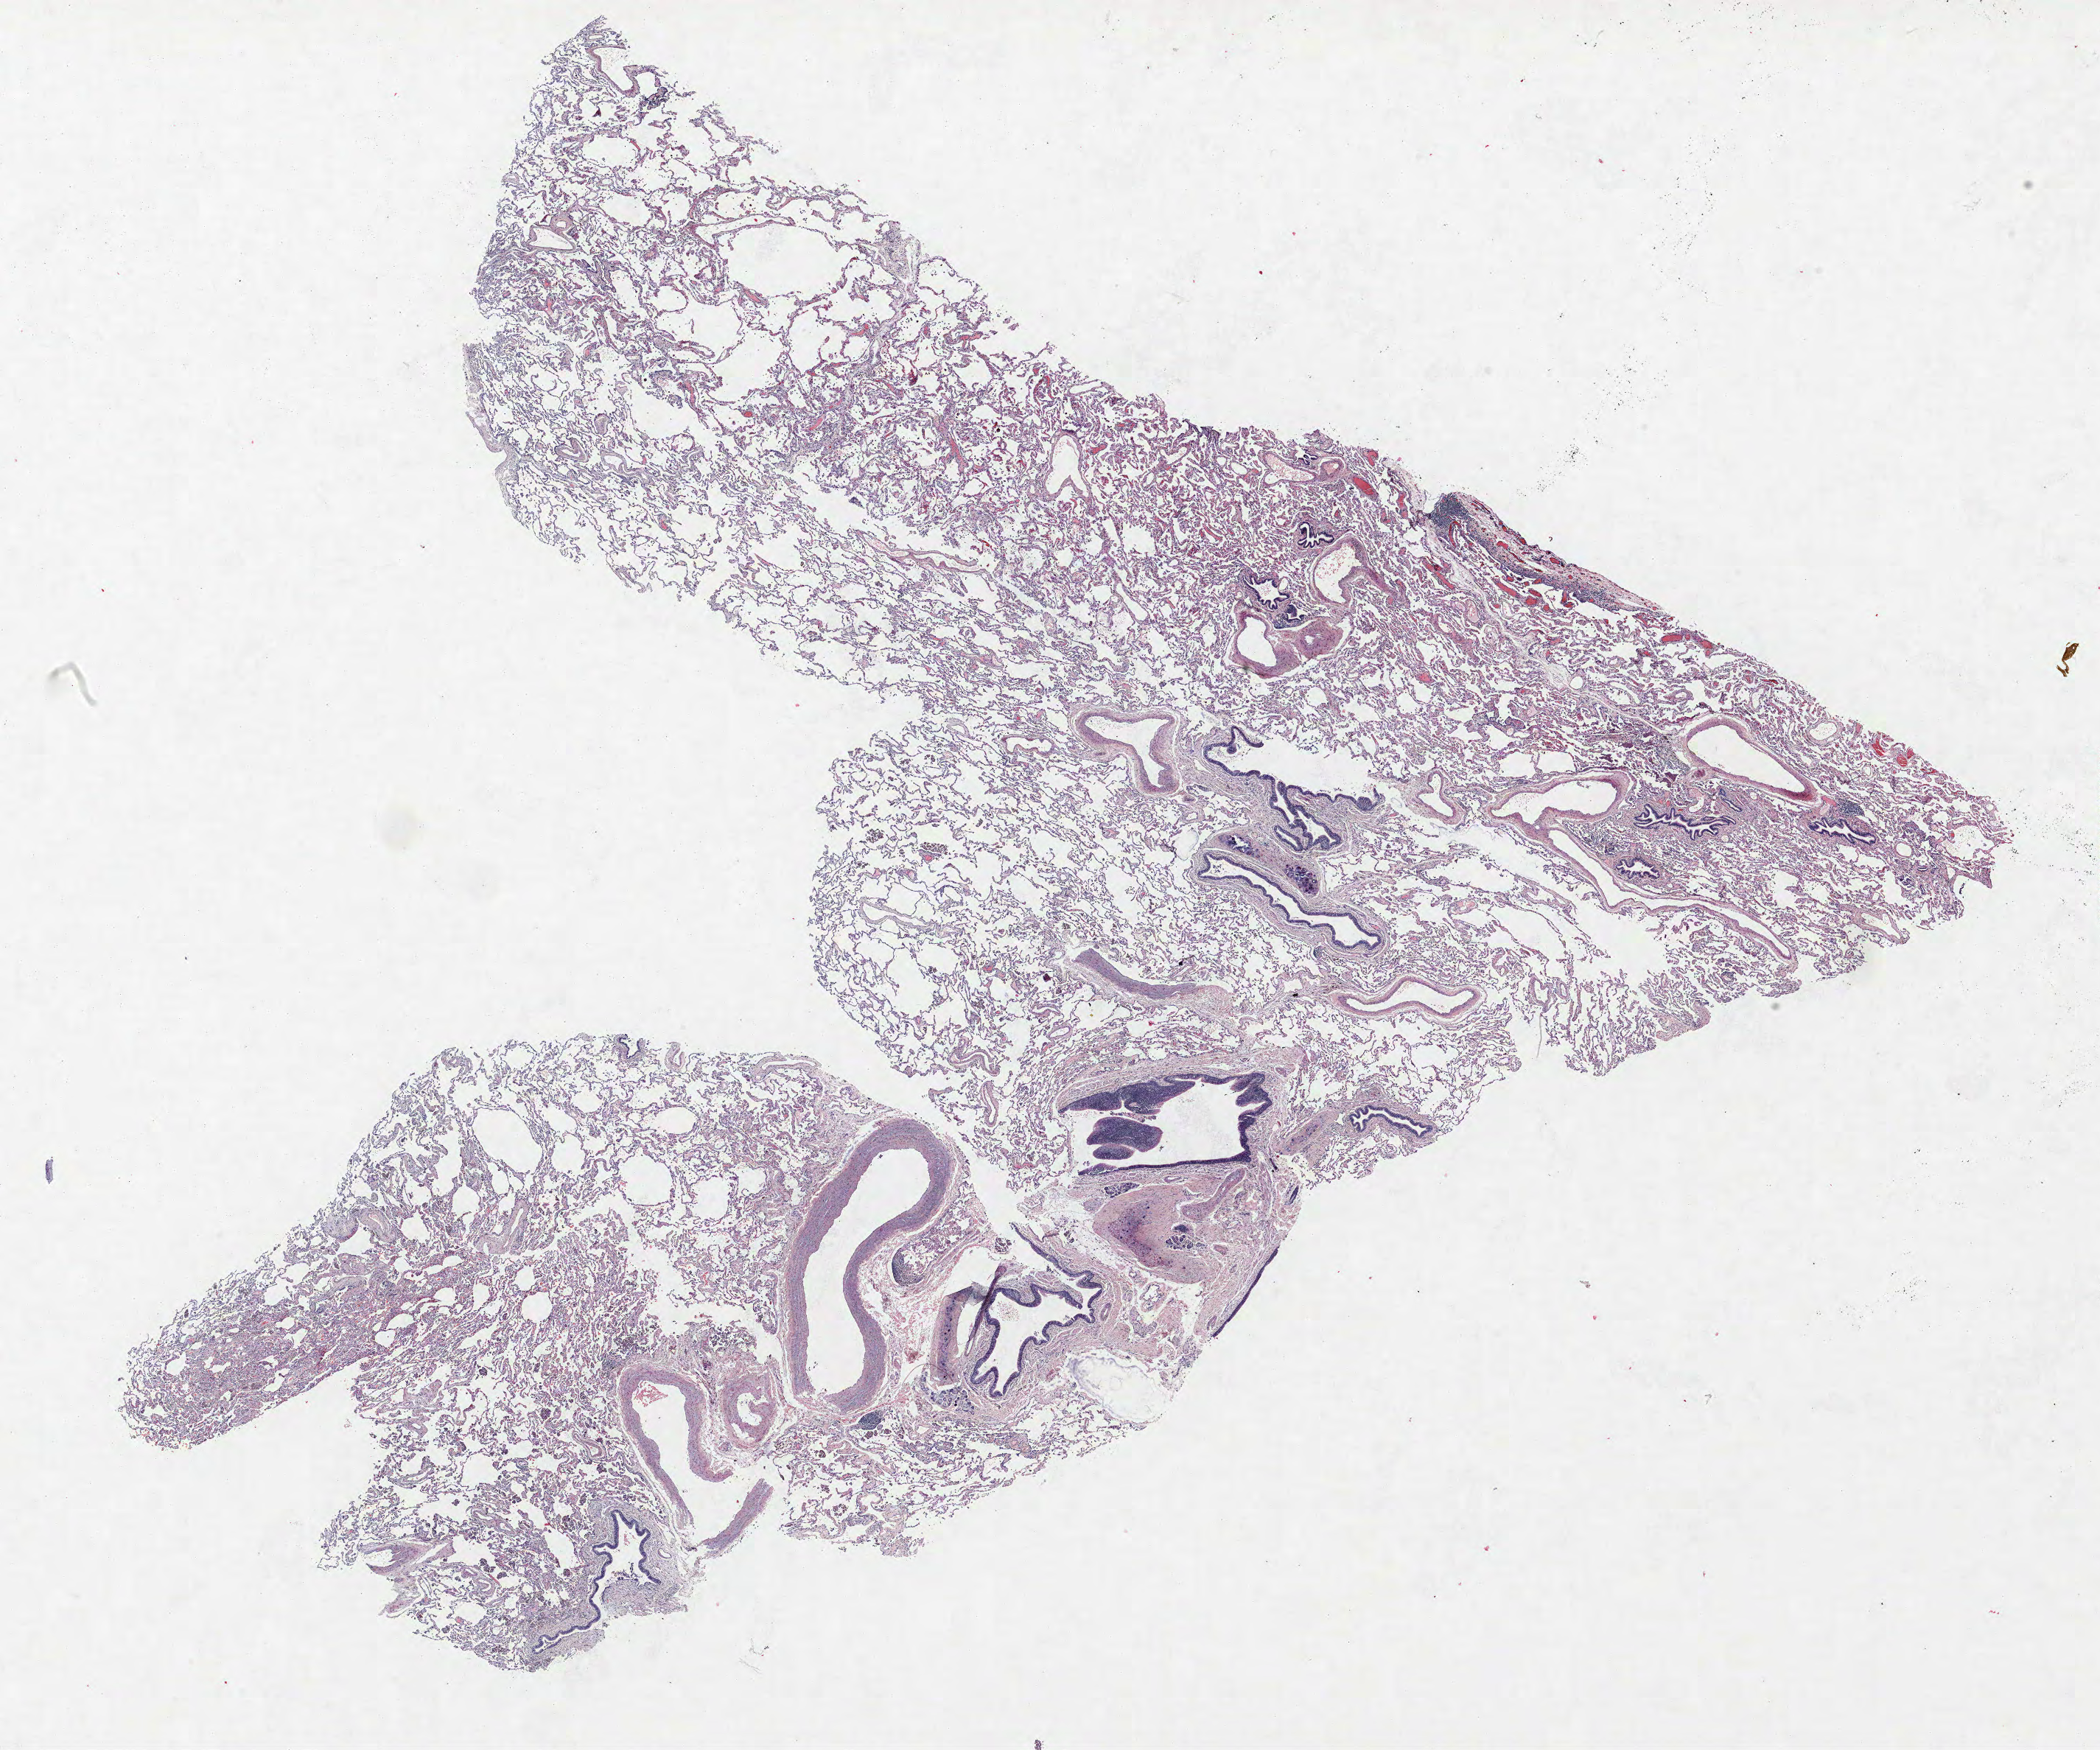
Whole-slide histology image, H&E — low-resolution overview of the scanned area, about 22.8 x 19.0 mm, FFPE section, lung tissue. Female patient, aged 68 at enrolment. Grade: well differentiated (G1).
* primary tumour location (clinical record): right lower lobe
* tumour size (pathology): 25 mm
* stage (AJCC 6th edition): IA
* participant's lung-cancer diagnosis: Adenocarcinoma, NOS